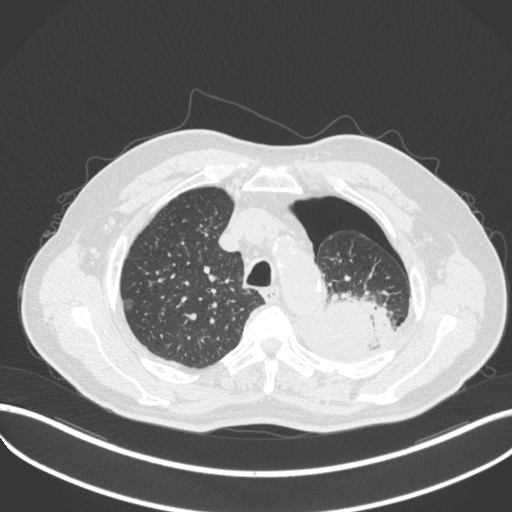
Chest CT, one axial slice; slice 398 of 466 in the series (ordered by position); 120 kVp; lung window (W 1500 / L -600 HU); 1 mm slice thickness; 512 × 512 image matrix. Male patient, age 76 years. From the clinical record (not read from this slice): clinical TNM (as recorded): T3 N0 M1b.
Structures marked on this image (rectangle marked by the reading radiologist):
- lung tumour (recorded histology: adenocarcinoma): bounding box [x1, y1, x2, y2] px = [311, 287, 376, 359]